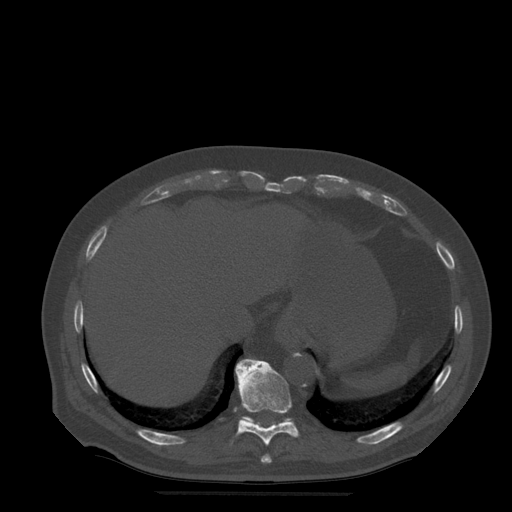
CT including the spine, one axial slice. Position 264 of 522 along the scan axis. Bone window (W 1800 / L 400 HU). 512 × 512 image matrix, field of view 420 × 420 mm. Patient age 72 years. From the clinical record (not read from this slice): primary cancer: prostate.
Outlined on this slice (semi-automatic segmentation, software-assisted and operator-edited):
- T10 vertebra: box from (x=236, y=359) to (x=300, y=446) px
- T11 vertebra: (x=242, y=361)–(x=291, y=425)
- T9 vertebra: (x=261, y=454)–(x=272, y=464)